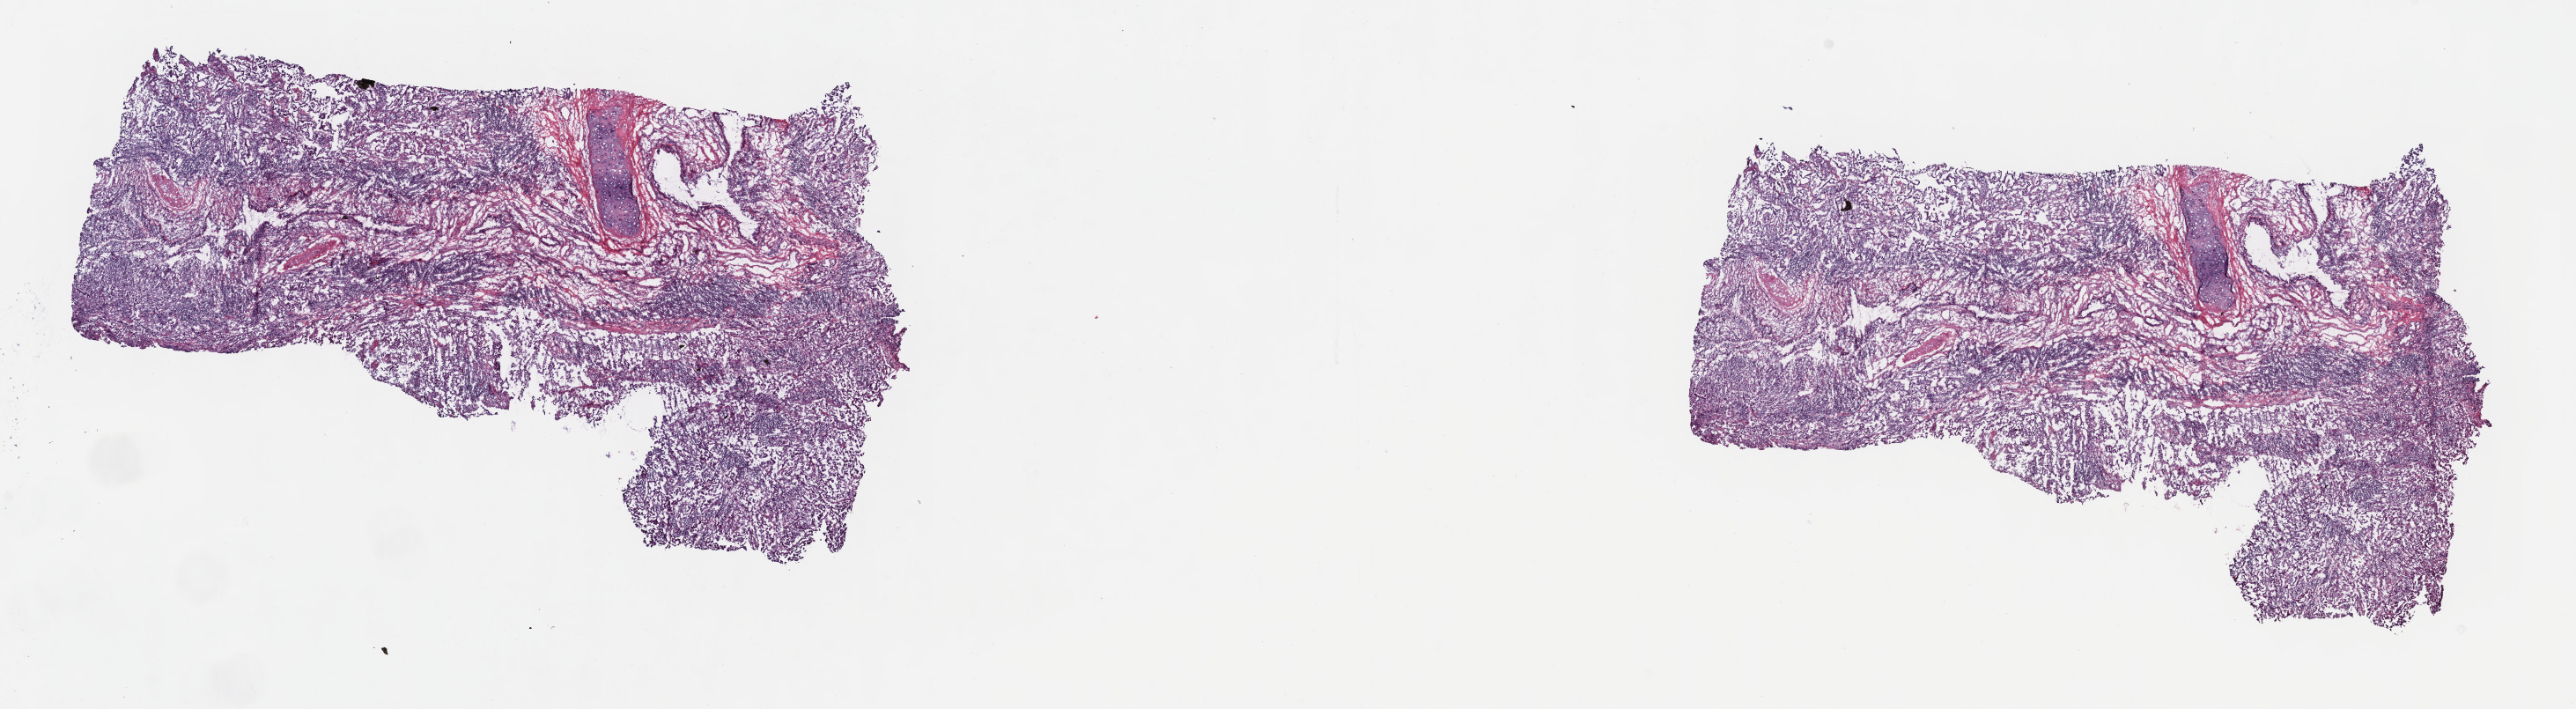
Hematoxylin and eosin (H&E) stained whole-slide image — shown as a low-resolution overview of the whole scanned area (about 23.7 x 6.5 mm, slide scanned at 40x); frozen section; lung, primary tumour sample. Male patient; age at initial diagnosis 51 years. Pathologist review of this section (percent, as recorded): tumour cells 65%, tumour nuclei 65%, normal cells 8%, stromal cells 25%, necrosis 2%. Infiltration values recorded for this section: lymphocyte infiltration 6%, monocyte infiltration 2%, neutrophil infiltration 5%.
Laterality: left. Diagnosis: Adenocarcinoma, NOS (upper lobe, lung). AJCC pathologic stage: IIIA (6th edition).